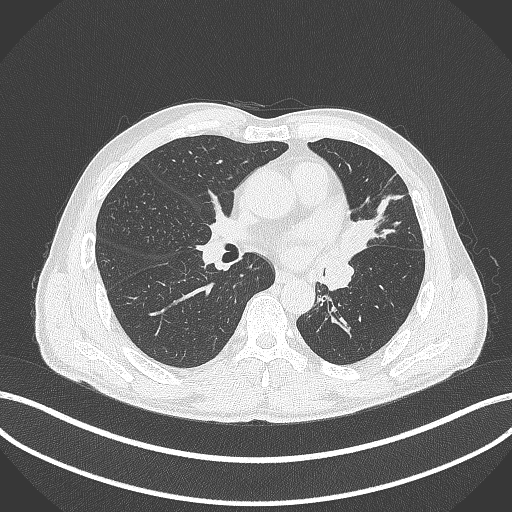
Chest CT, one axial slice. Position 223 of 429 along the scan axis. Lung window (W 1500 / L -600 HU). 1 mm slice thickness. 512 × 512 image matrix, field of view 400 × 400 mm. Male patient, age 57 years. Case-level facts recorded for this patient, not image findings: clinical TNM (as recorded): T2b N0 M0.
Structures marked on this image (bounding box drawn by a radiologist):
- lung tumour (recorded histology: squamous cell carcinoma): box from (x=339, y=210) to (x=374, y=263) px